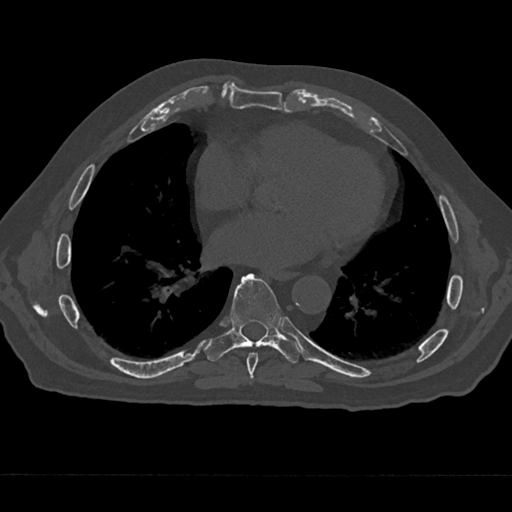
CT including the spine, one axial slice; 120 kVp; bone window (W 1800 / L 400 HU); 0.5 mm slice thickness; 512 × 512 image matrix, field of view 377 × 377 mm. Patient: male, 75 years. From the clinical record (not read from this slice): primary cancer: renal.
Annotated regions visible in this slice (semi-automatic segmentation, software-assisted and operator-edited):
- T7 vertebra: bounding box [x1, y1, x2, y2] px = [244, 352, 259, 379]
- T8 vertebra: [204, 273, 301, 363]